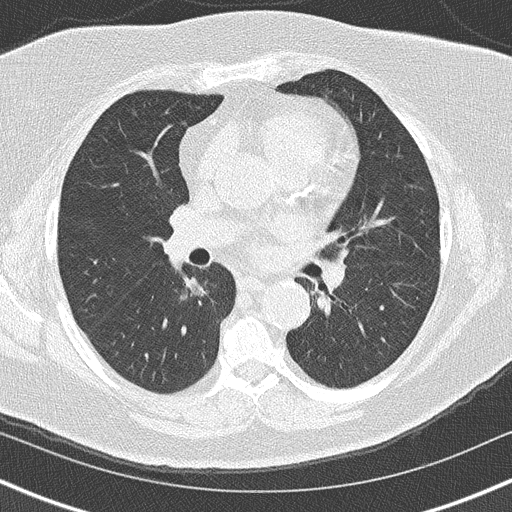
Low-dose screening chest CT, axial slice; second annual screen; lung window (W 1500 / L -600 HU); 2 mm slice thickness; lung (sharp) reconstruction kernel (B50f); slice 66 of 152 in the series. Female participant, aged 60 years at enrolment. Former smoker at enrolment.
Expert reader's lesion annotation, box from (x=150, y=263) to (x=211, y=320) px. The exam's reader record, not a measurement of the box and not confirmed to be the same lesion: non-calcified nodule or mass ≥4 mm, right lower lobe, 20 × 19 mm, soft tissue attenuation, pre-existing on the prior screen: yes; interval growth: yes. Official screen result: positive, other. Participant outcome: lung cancer diagnosed 139 days after this screen — bronchiolo-alveolar carcinoma, non-mucinous, right lower lobe, stage IA (AJCC 6th edition), 15 mm at pathology.